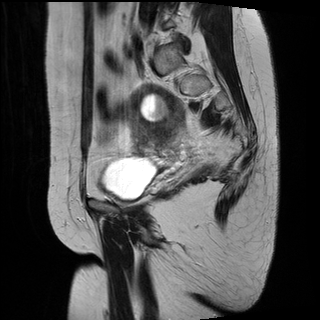
Pelvic MRI for cervical cancer, one sagittal slice. Position 22 of 34 along the scan axis. T2-weighted. 1.5 T. TE 89 ms, TR 3320 ms. 4 mm slice thickness. 320 × 320 image matrix. Female patient, age 49 years.
Outlined on this slice (expert manual segmentation):
- uterus and cervix: bounding box <126,84,185,147> (left, top, right, bottom; pixels)